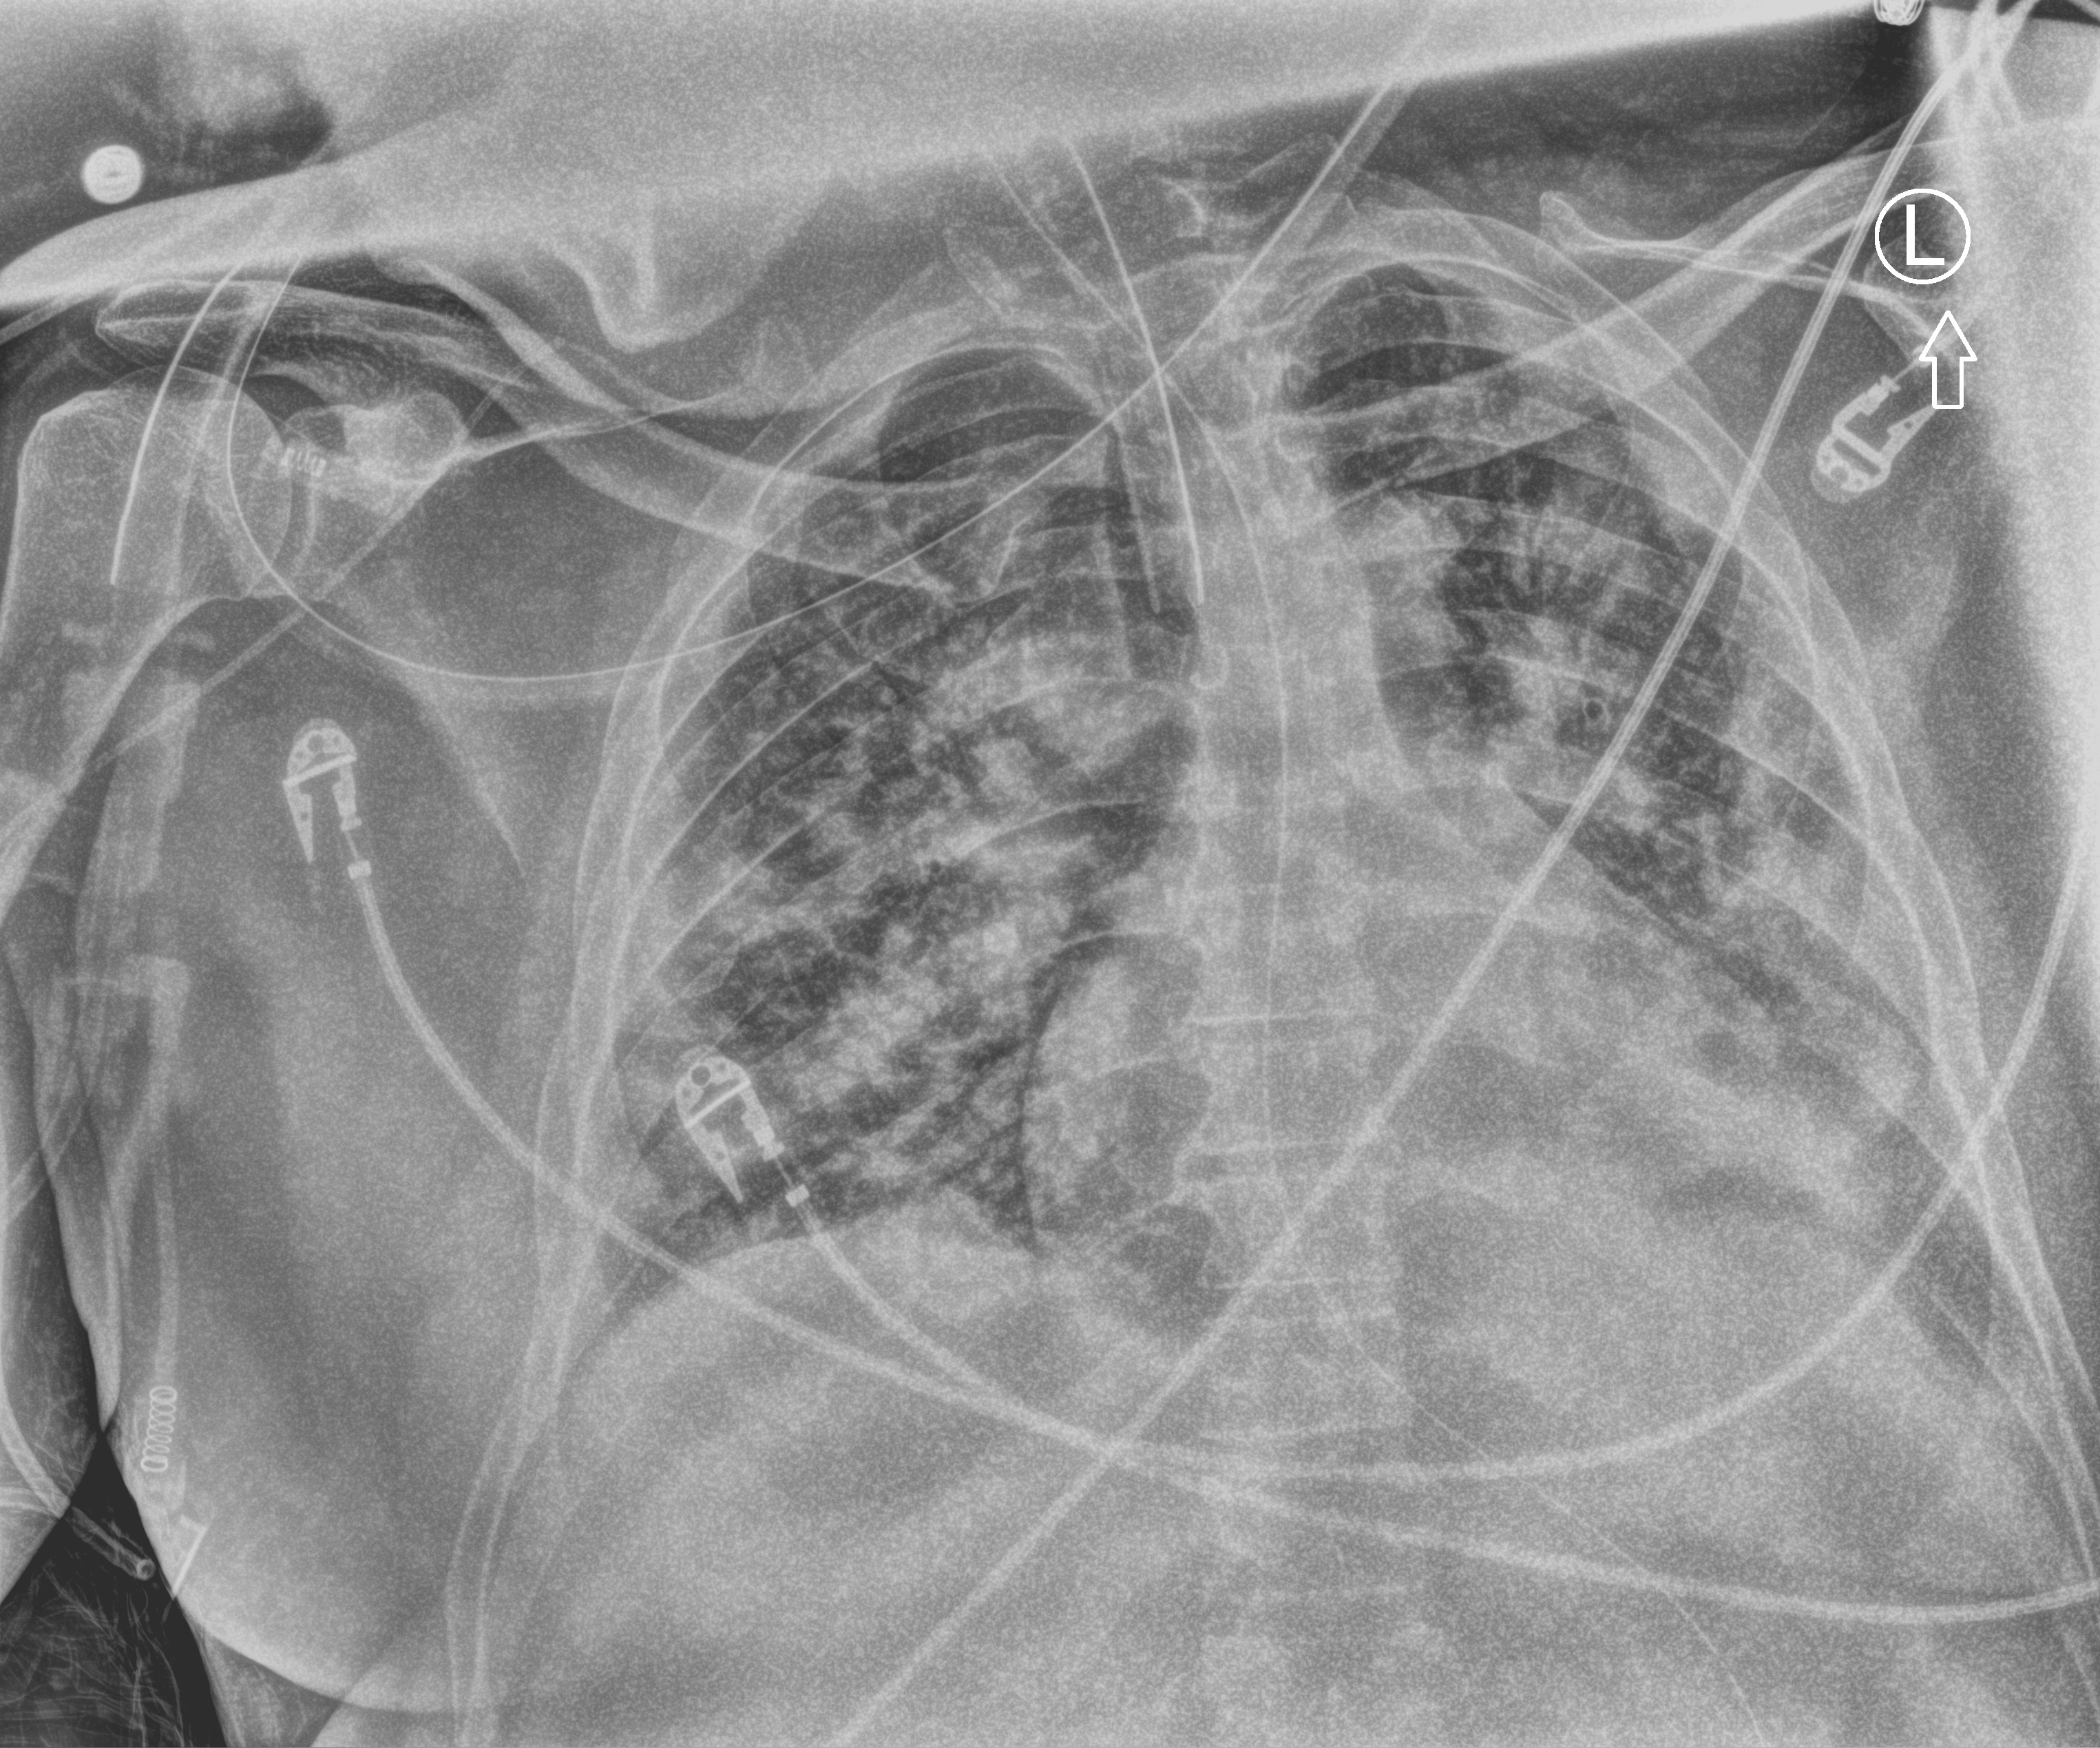
Chest X-ray (portable), anteroposterior (AP) projection. Male patient hospitalised with COVID-19, age 18–59 years.
Admission-level facts for this patient (not findings on this image; timing relative to this image not recorded): chronic kidney disease (admission record): no.